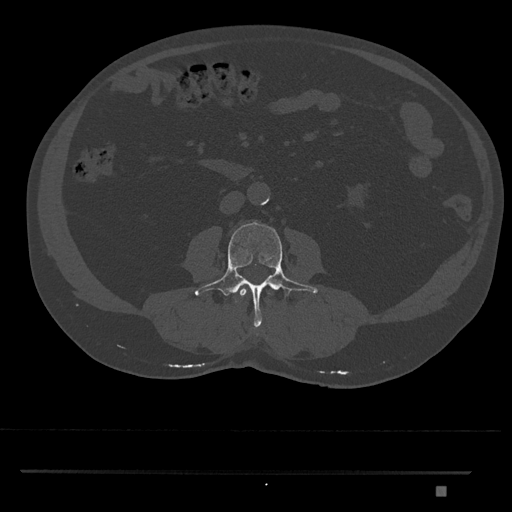
CT including the spine, one axial slice; slice 686 of 1134 in the series (ordered by position); 120 kVp; bone window (W 1800 / L 400 HU); 512 × 512 image matrix, field of view 429 × 429 mm. Patient: male, 65 years. Case-level facts recorded for this patient, not image findings: primary cancer: prostate.
Outlined on this slice (semi-automatic segmentation, software-assisted and operator-edited):
- L2 vertebra: bounding box (x1, y1, x2, y2) in pixels: (239, 287, 271, 298)
- L3 vertebra: (194, 221, 318, 335)